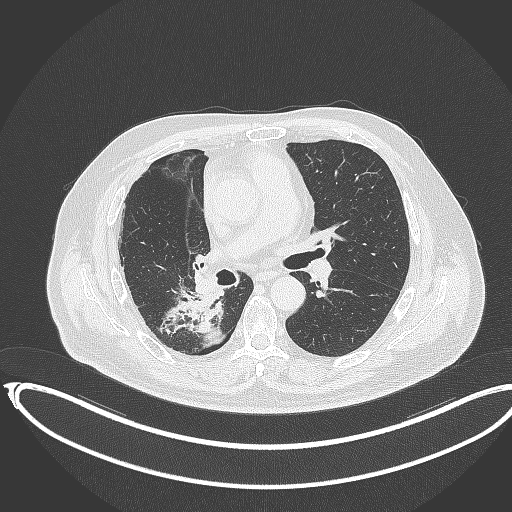
Chest CT, one axial slice; position 193 of 403 along the scan axis; reconstruction kernel B70f; 120 kVp; lung window (W 1500 / L -600 HU); 1 mm slice thickness; 512 × 512 image matrix, field of view 436 × 436 mm. Patient: male, 68 years. Case-level facts recorded for this patient, not image findings: clinical TNM (as recorded): T2a N0 M0.
Structures marked on this image (rectangle marked by the reading radiologist):
- lung tumour (recorded histology: adenocarcinoma): bounding box <166,289,233,348> (left, top, right, bottom; pixels)